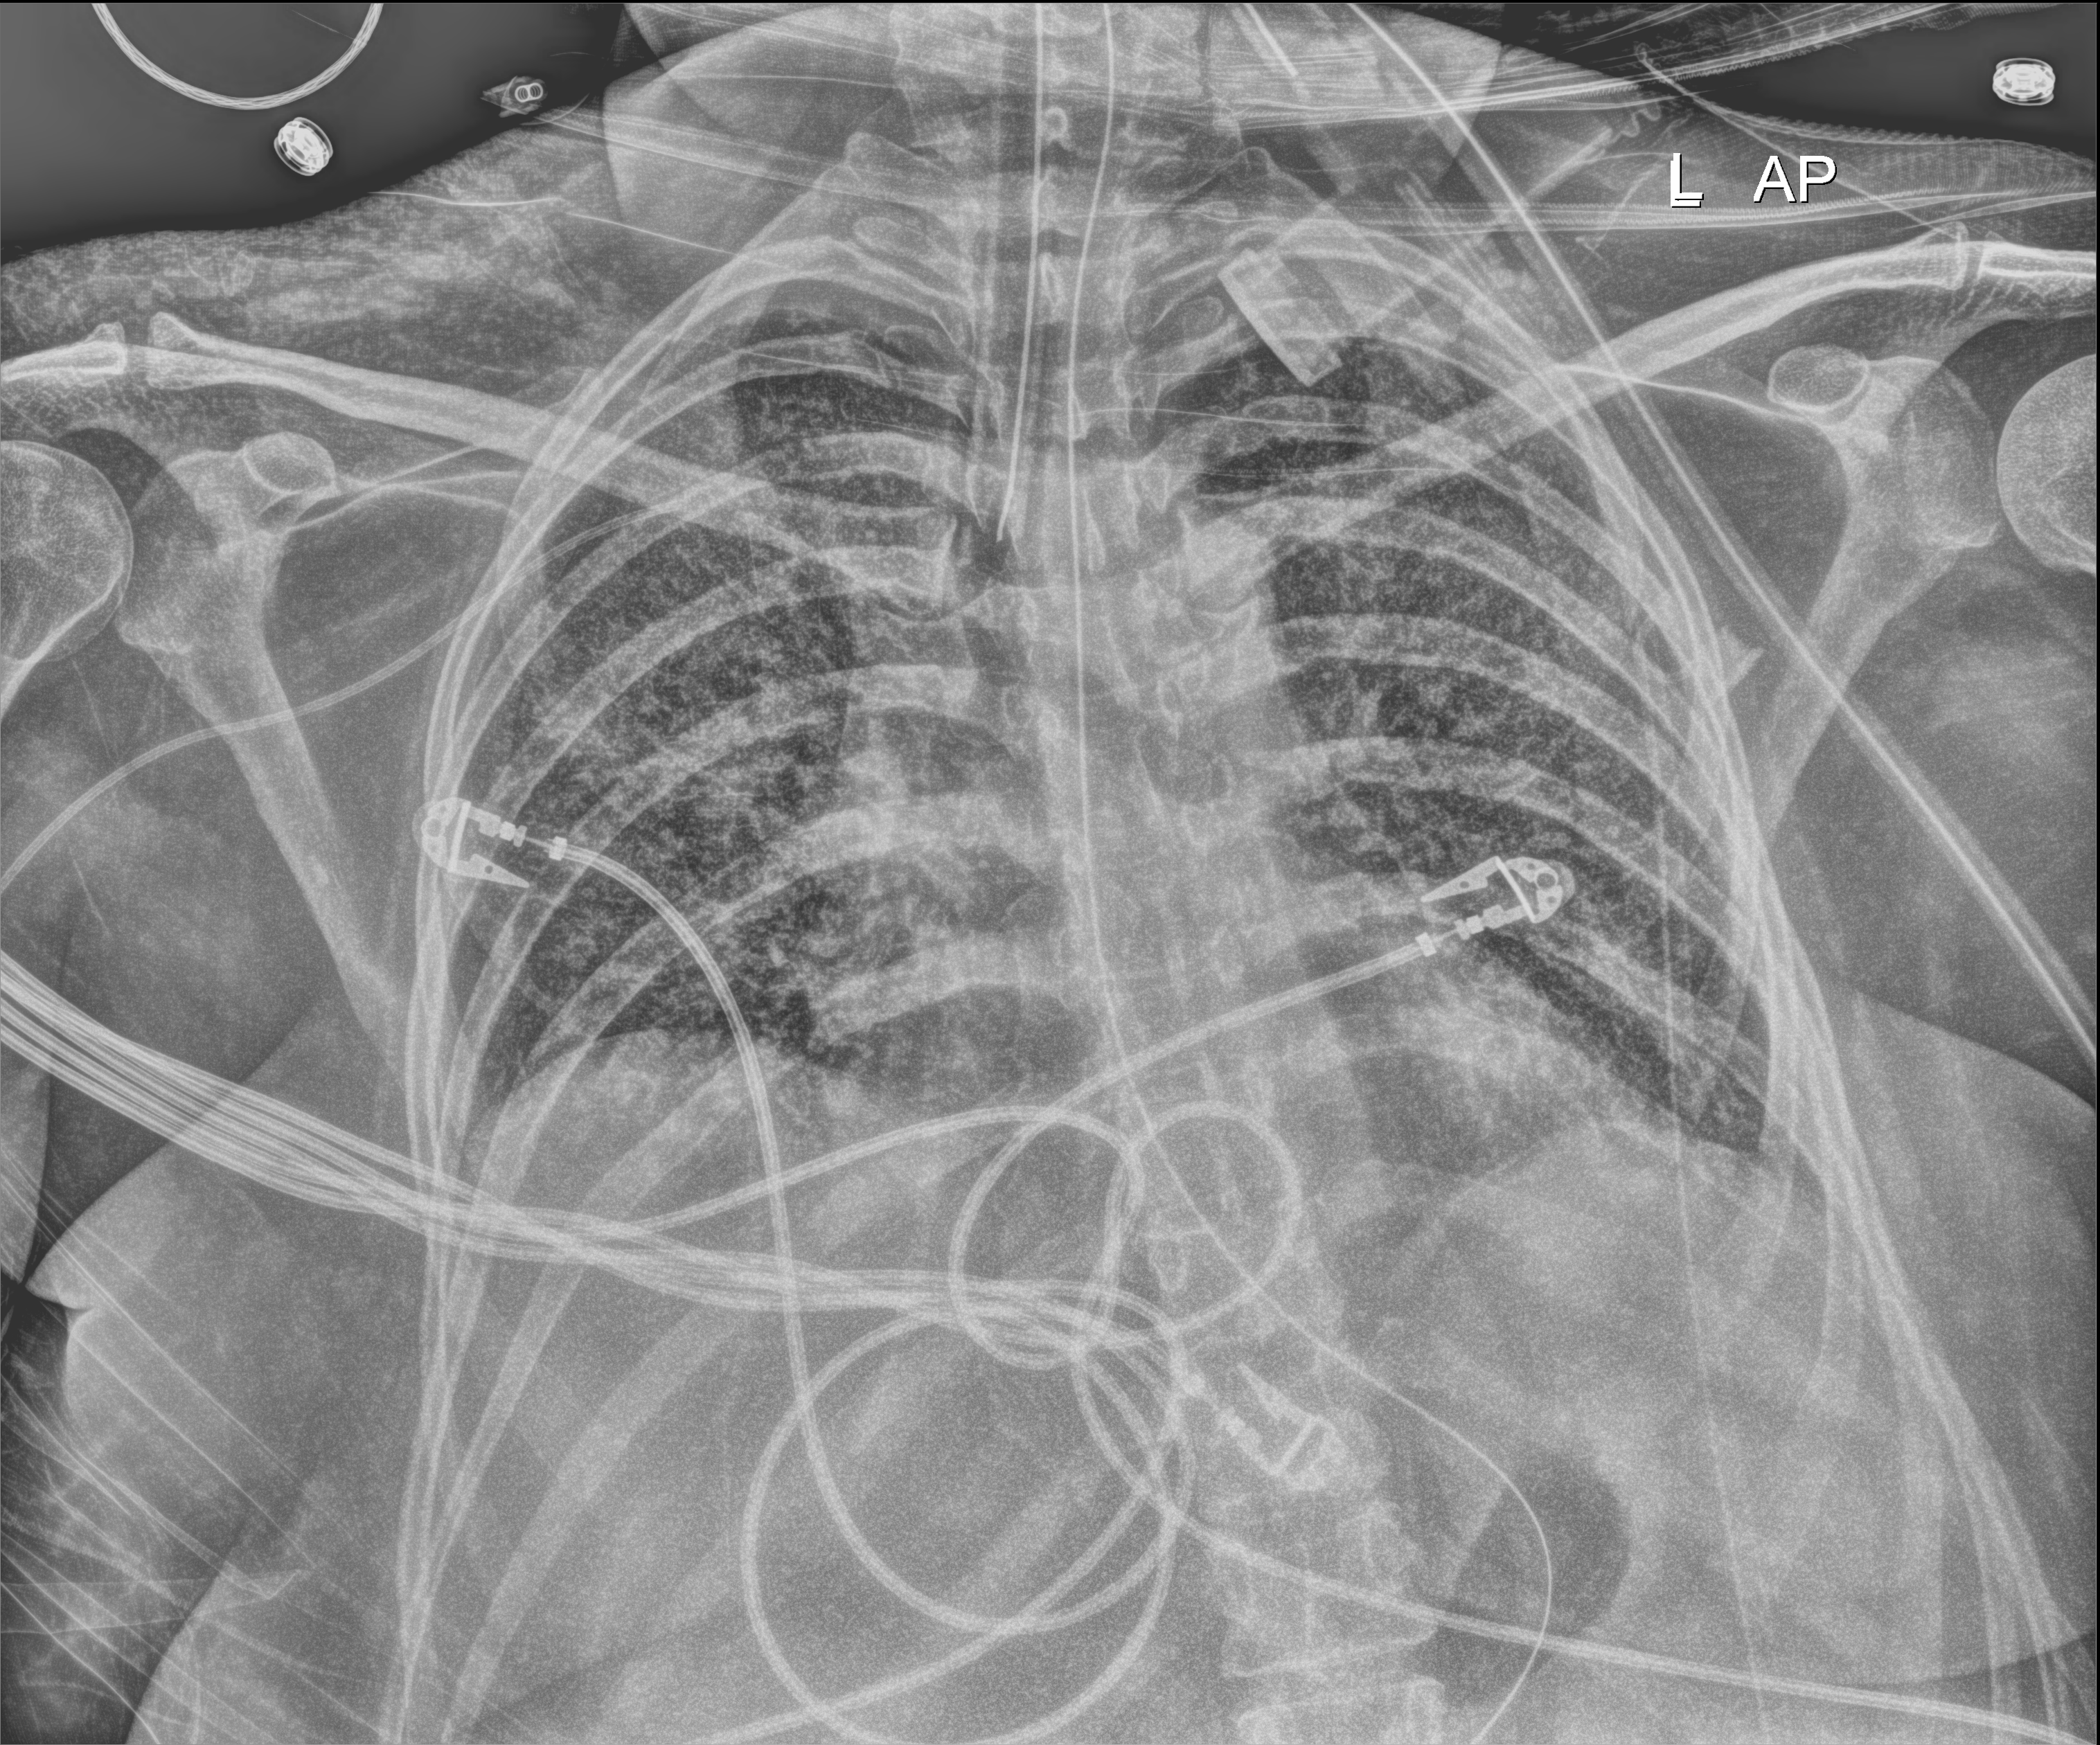
Bedside chest radiograph (digital radiography). Patient hospitalised with COVID-19; female, aged 18–59 years.
From the hospital-stay record, not from the radiograph (when in the stay this image was taken is not recorded): smoking status (admission record): former; mechanically ventilated during this hospital stay: yes; admitted to intensive care during this hospital stay: yes.